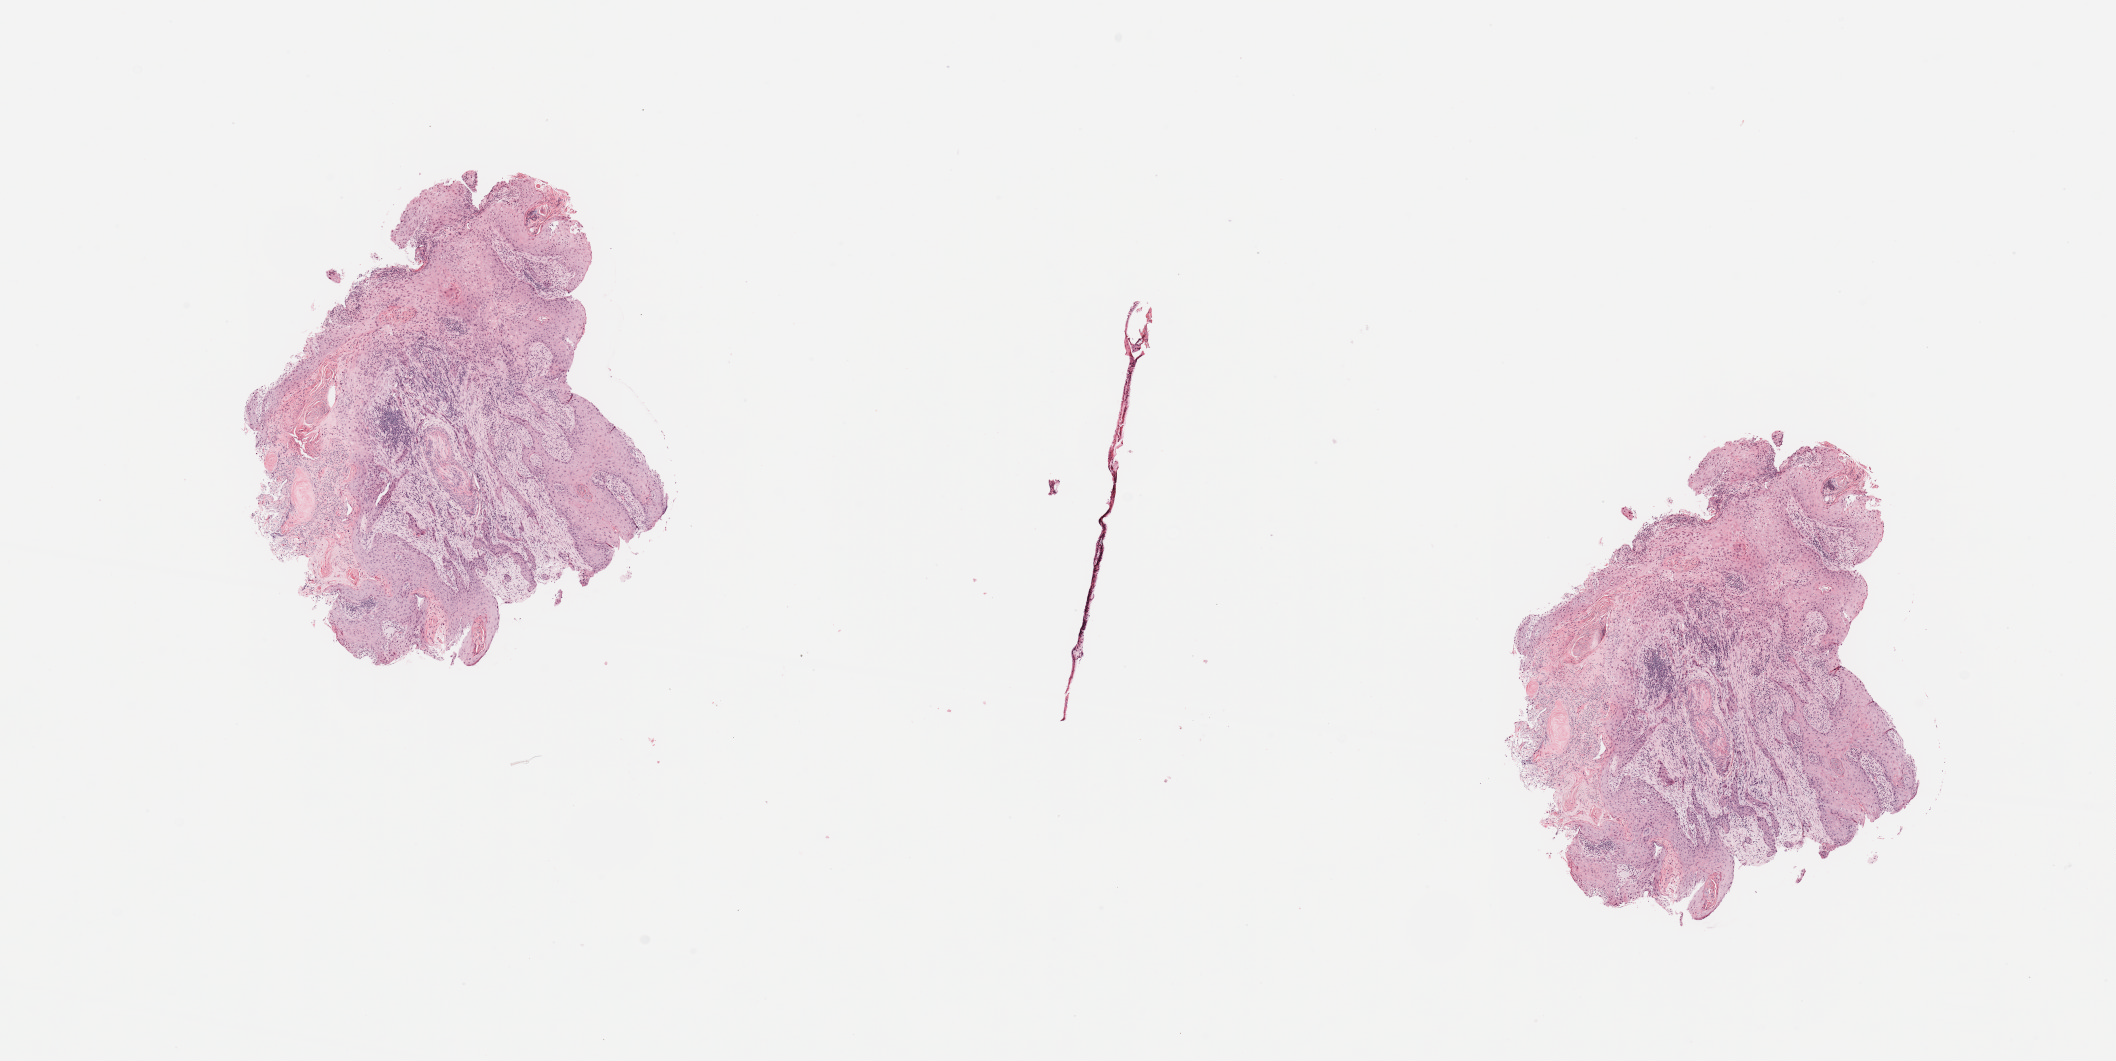
Digitized Hematoxylin and eosin (H&E) stained tissue section (whole slide), shown as a low-resolution overview of the whole scanned area (about 16.7 x 8.4 mm, slide scanned at 20x), head and neck, tissue type not recorded. Female, 67 y/o.
- patient diagnosis: Squamous cell carcinoma, NOS (overlapping lesion of lip, oral cavity and pharynx)